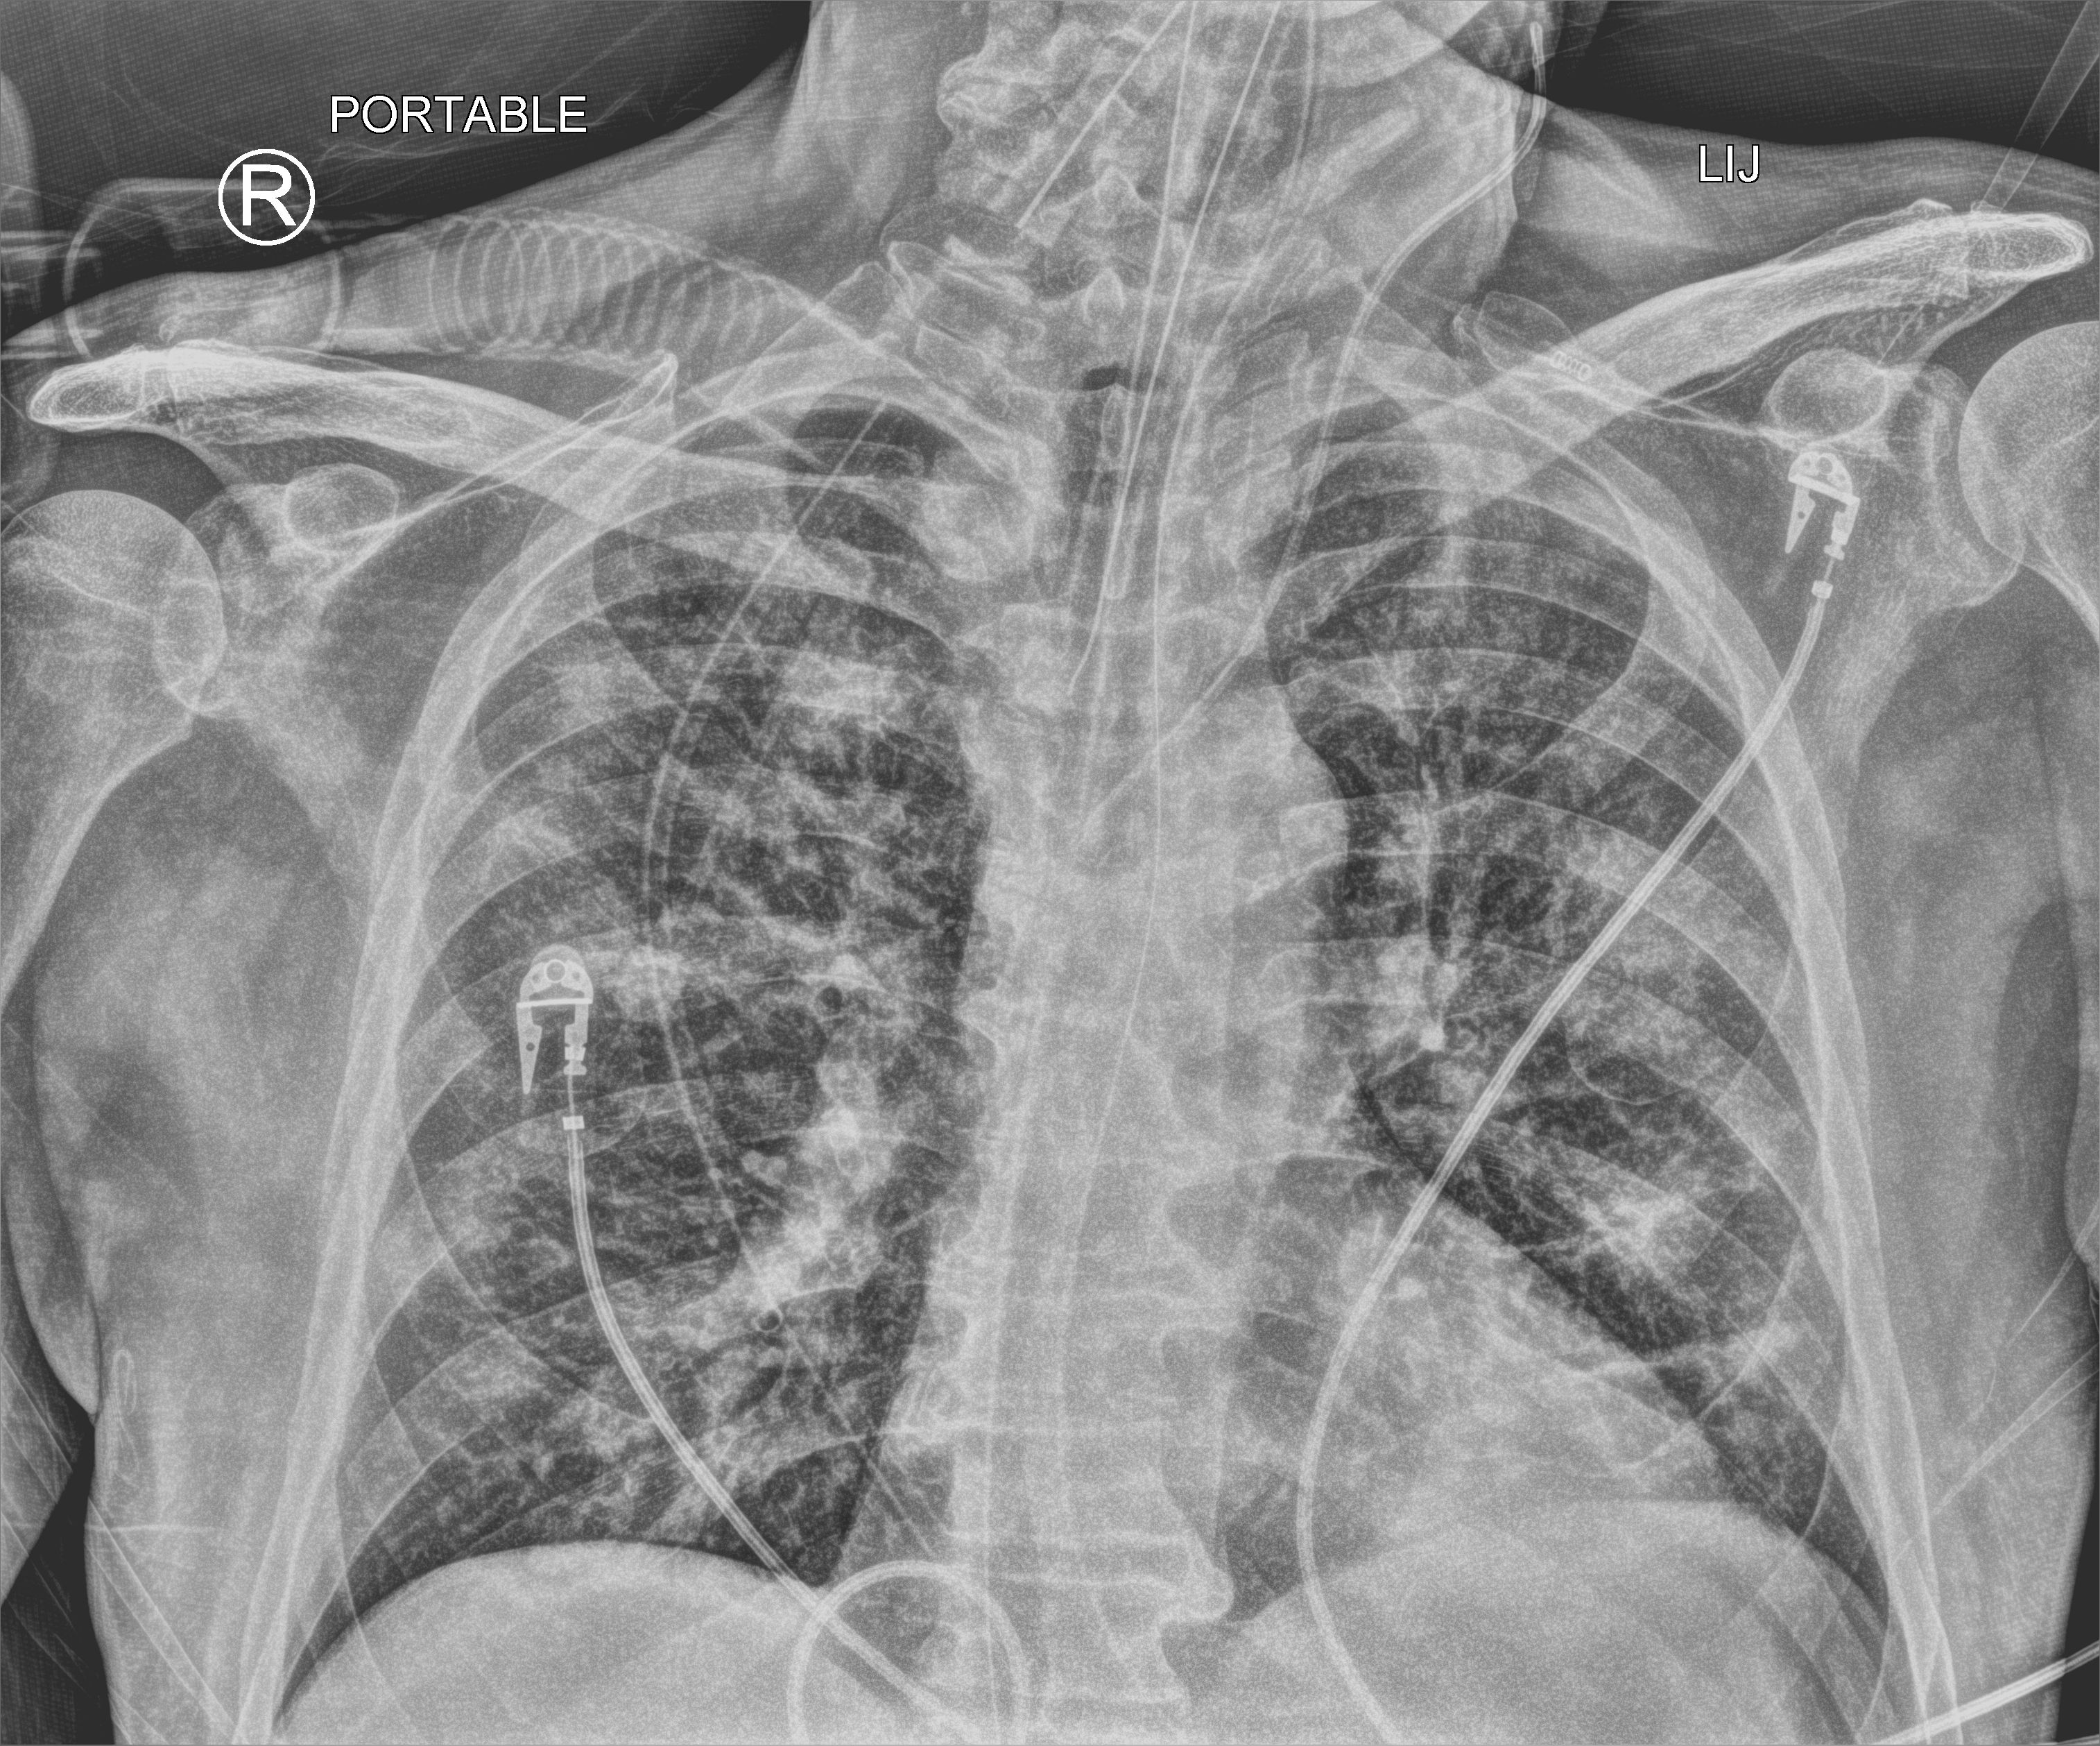
Chest X-ray (portable), anteroposterior (AP) projection. Patient hospitalised with COVID-19; male, aged 60–74 years.
Hospital-stay facts (about this admission, not read from this image; timing relative to this image not recorded):
- mechanically ventilated during this hospital stay: yes
- admitted to intensive care during this hospital stay: yes